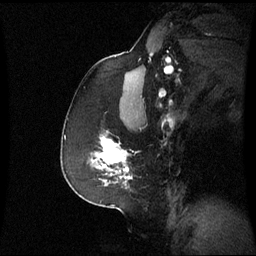
Breast MRI (dynamic contrast-enhanced), one sagittal slice. Dynamic contrast-enhanced series, image 2 of 3 at this slice position (ordered by acquisition). 1.5 T. TE 4.2 ms, TR 8.9 ms. 2.4 mm slice thickness. 256 × 256 image matrix. Female patient, age 59 years. From the clinical record (not read from this slice): setting: breast cancer imaged before/during neoadjuvant chemotherapy; receptor status: triple-negative.
Outlined on this slice (semi-automatic segmentation, software-assisted and operator-edited):
- analysis volume of interest (the breast-tissue region the enhancement analysis was run in; not a lesion): box from (x=88, y=137) to (x=133, y=183) px
- tumour enhancement mask (voxels above the 70 % enhancement threshold inside the analysis volume of interest): (x=99, y=137)–(x=131, y=179)